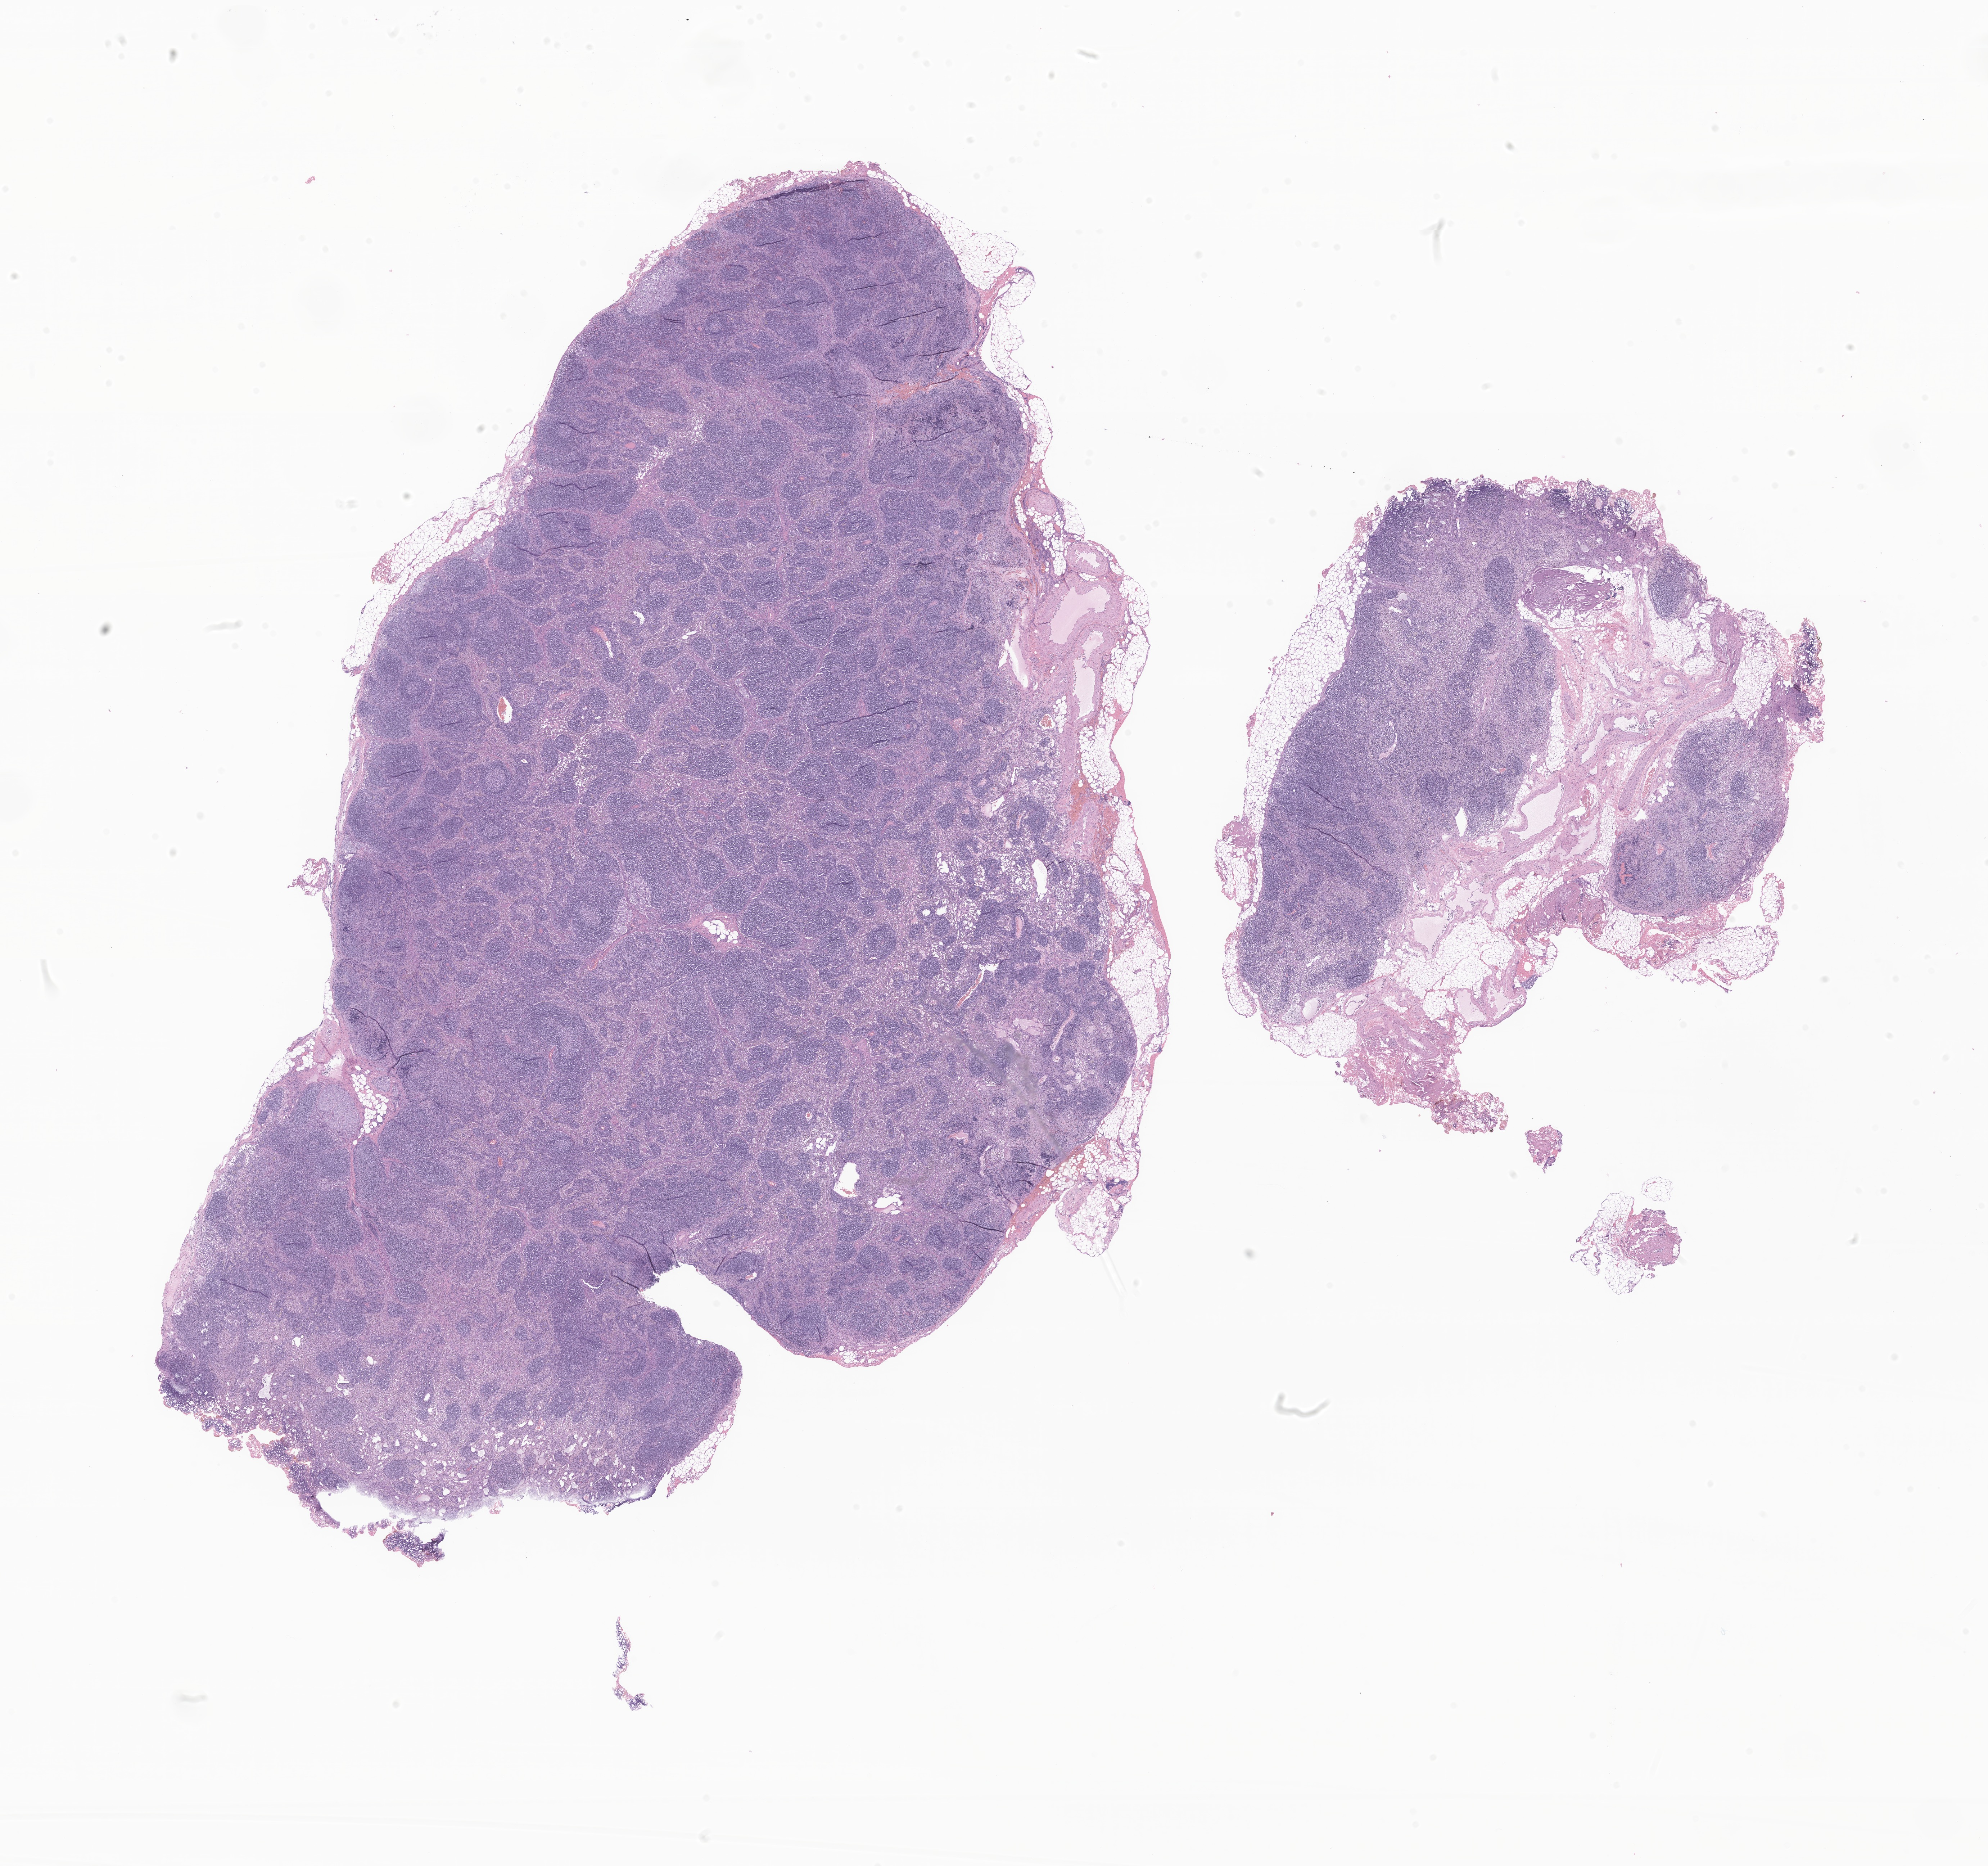
Whole-slide image, hematoxylin and eosin (H&E) stain of tumor tissue from the head of pancreas, shown as a low-resolution overview of the whole scanned area (about 23.3 x 21.9 mm); formalin-fixed paraffin-embedded section. Female patient, age 224 months (18 years 8 months).
- diagnosis (ICD-O-3 morphology term): Neuroendocrine tumor, NOS